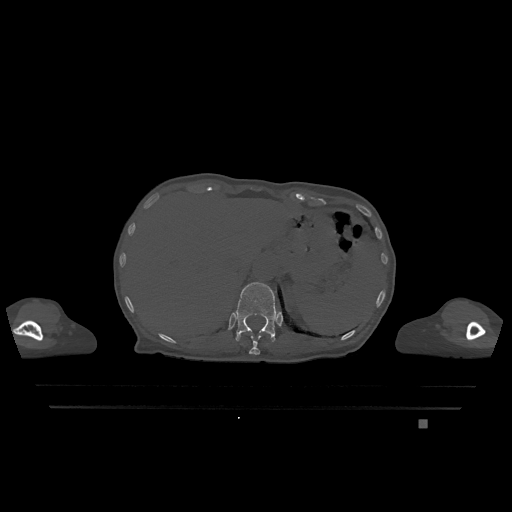
CT including the spine, one axial slice. Slice 549 of 1317 in the series (ordered by position). Bone window (W 1800 / L 400 HU). 0.5 mm slice thickness. 512 × 512 image matrix. Patient: female, 74 years. From the clinical record (not read from this slice): primary cancer: lung; vertebrae with lytic lesions (as recorded): T1, T4, T5, T6, L4, L5.
Annotated regions visible in this slice (semi-automatic segmentation, software-assisted and operator-edited):
- T11 vertebra: bounding box <249,333,268,355> (left, top, right, bottom; pixels)
- T12 vertebra: <236,282,278,342>